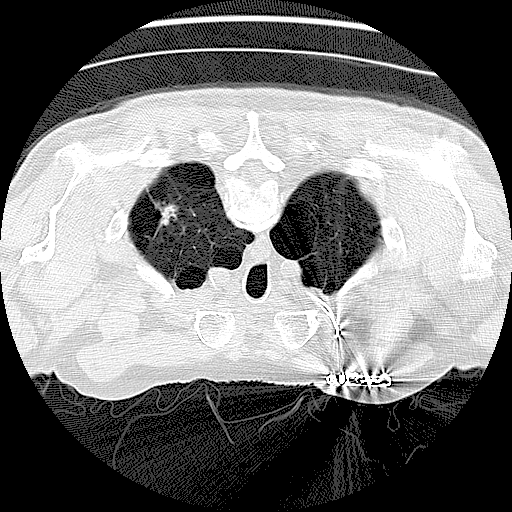
Axial slice from a low-dose chest CT screening exam, baseline screening round, lung window (W 1500 / L -600 HU), 2.5 mm slice thickness, lung (sharp) reconstruction kernel (LUNG), 120 kVp, slice 20 of 138 in the series. Male, age 73 years at enrolment. Current smoker at enrolment.
• Expert reader's lesion annotation, bounding box (x1, y1, x2, y2) in pixels: (141, 191, 186, 237).
• The screening reader recorded 2 non-calcified nodules or masses ≥4 mm on this exam (left lower lobe, right middle lobe); which of them this box marks is not recorded.
• Participant outcome: lung cancer diagnosed 308 days after this screen — neoplasm, malignant, stage IV (AJCC 6th edition).